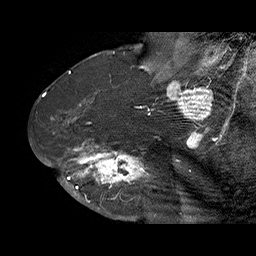
Breast MRI (dynamic contrast-enhanced), one sagittal slice; slice 42 of 70 in the series (ordered by position); dynamic contrast-enhanced series, time point 2 of 6 at this slice position (early post-contrast); 1.5 T; TE 4.5 ms, TR 32.4 ms; 3 mm slice thickness; 256 × 256 image matrix, field of view 180 × 180 mm. Female patient. From the clinical record (not read from this slice): setting: breast cancer imaged before/during neoadjuvant chemotherapy; receptor status: HR-positive, HER2-negative.
Annotated regions visible in this slice (semi-automatic segmentation, software-assisted and operator-edited):
- analysis volume of interest (the breast-tissue region the enhancement analysis was run in; not a lesion): bounding box [x1, y1, x2, y2] px = [71, 128, 159, 202]
- tumour enhancement mask (voxels above the 100 % enhancement threshold inside the analysis volume of interest): [71, 138, 151, 202]